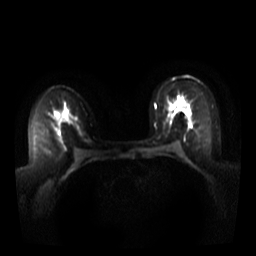
Breast MRI, one axial slice. Slice 19 of 44 in the series (ordered by position). Diffusion-weighted series; image 2 of 4 stored at this slice position (different b-values; order by instance number). 3 T. 256 × 256 image matrix, field of view 340 × 340 mm. Female patient.
Annotated regions visible in this slice (manually delineated by an expert):
- tumour on diffusion-weighted imaging: bounding box [x1, y1, x2, y2] px = [178, 104, 188, 113]